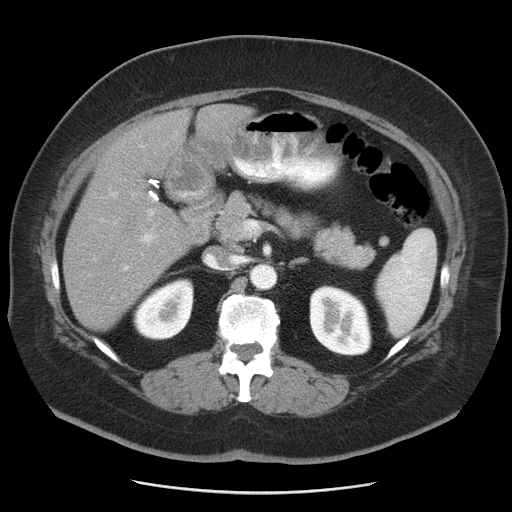
Contrast-enhanced abdominal CT, one axial slice; position 25 of 55 along the scan axis; 120 kVp; intravenous contrast given; soft-tissue window (W 400 / L 40 HU); 5 mm slice thickness; 512 × 512 image matrix, field of view 380 × 380 mm. Female patient, age 52 years. From the clinical record (not read from this slice): diagnosis: colorectal cancer liver metastases, imaged before liver resection; multiple liver metastases: yes; largest metastasis: 2.5 cm; disease in both lobes: yes.
Annotated regions visible in this slice (outlined manually by an expert reader):
- liver: bounding box [x1, y1, x2, y2] px = [63, 105, 252, 329]
- planned liver remnant (the part of the liver to remain after resection): [63, 197, 193, 329]
- portal vein (with intrahepatic branches): [93, 144, 159, 272]